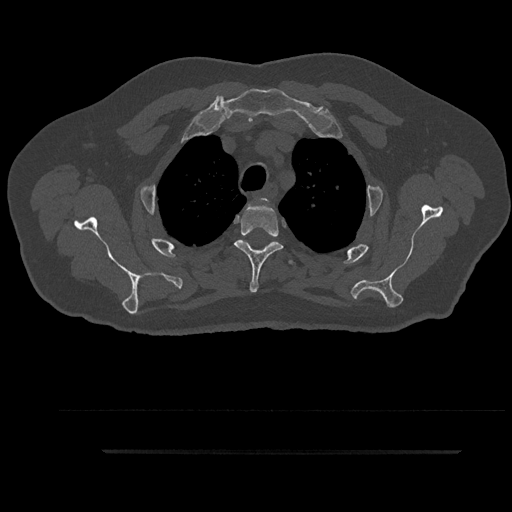
CT including the spine, one axial slice; 120 kVp; bone window (W 1800 / L 400 HU); 0.5 mm slice thickness; 512 × 512 image matrix, field of view 432 × 432 mm. Male patient, age 63 years. From the clinical record (not read from this slice): primary cancer: renal.
Outlined on this slice (semi-automatic segmentation, software-assisted and operator-edited):
- T2 vertebra: bounding box (x1, y1, x2, y2) in pixels: (254, 198, 271, 205)
- T3 vertebra: (234, 204, 283, 293)
- T4 vertebra: (288, 259, 296, 267)